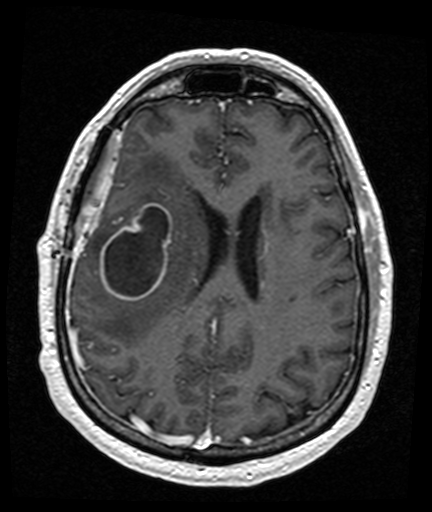
Brain MRI from a brain-tumour surgery series, one axial slice. Slice 61 of 176 in the series (ordered by position). T1-weighted post-contrast. 1 mm slice thickness. 432 × 512 image matrix. From the clinical record (not read from this slice): histopathology: Glioblastoma; WHO grade: 4; IDH mutation: no; tumour location: Right Frontal Temporal, Posterior Sylvian Fissure.
Outlined on this slice (expert manual segmentation):
- tumour: bounding box <101,203,173,301> (left, top, right, bottom; pixels)